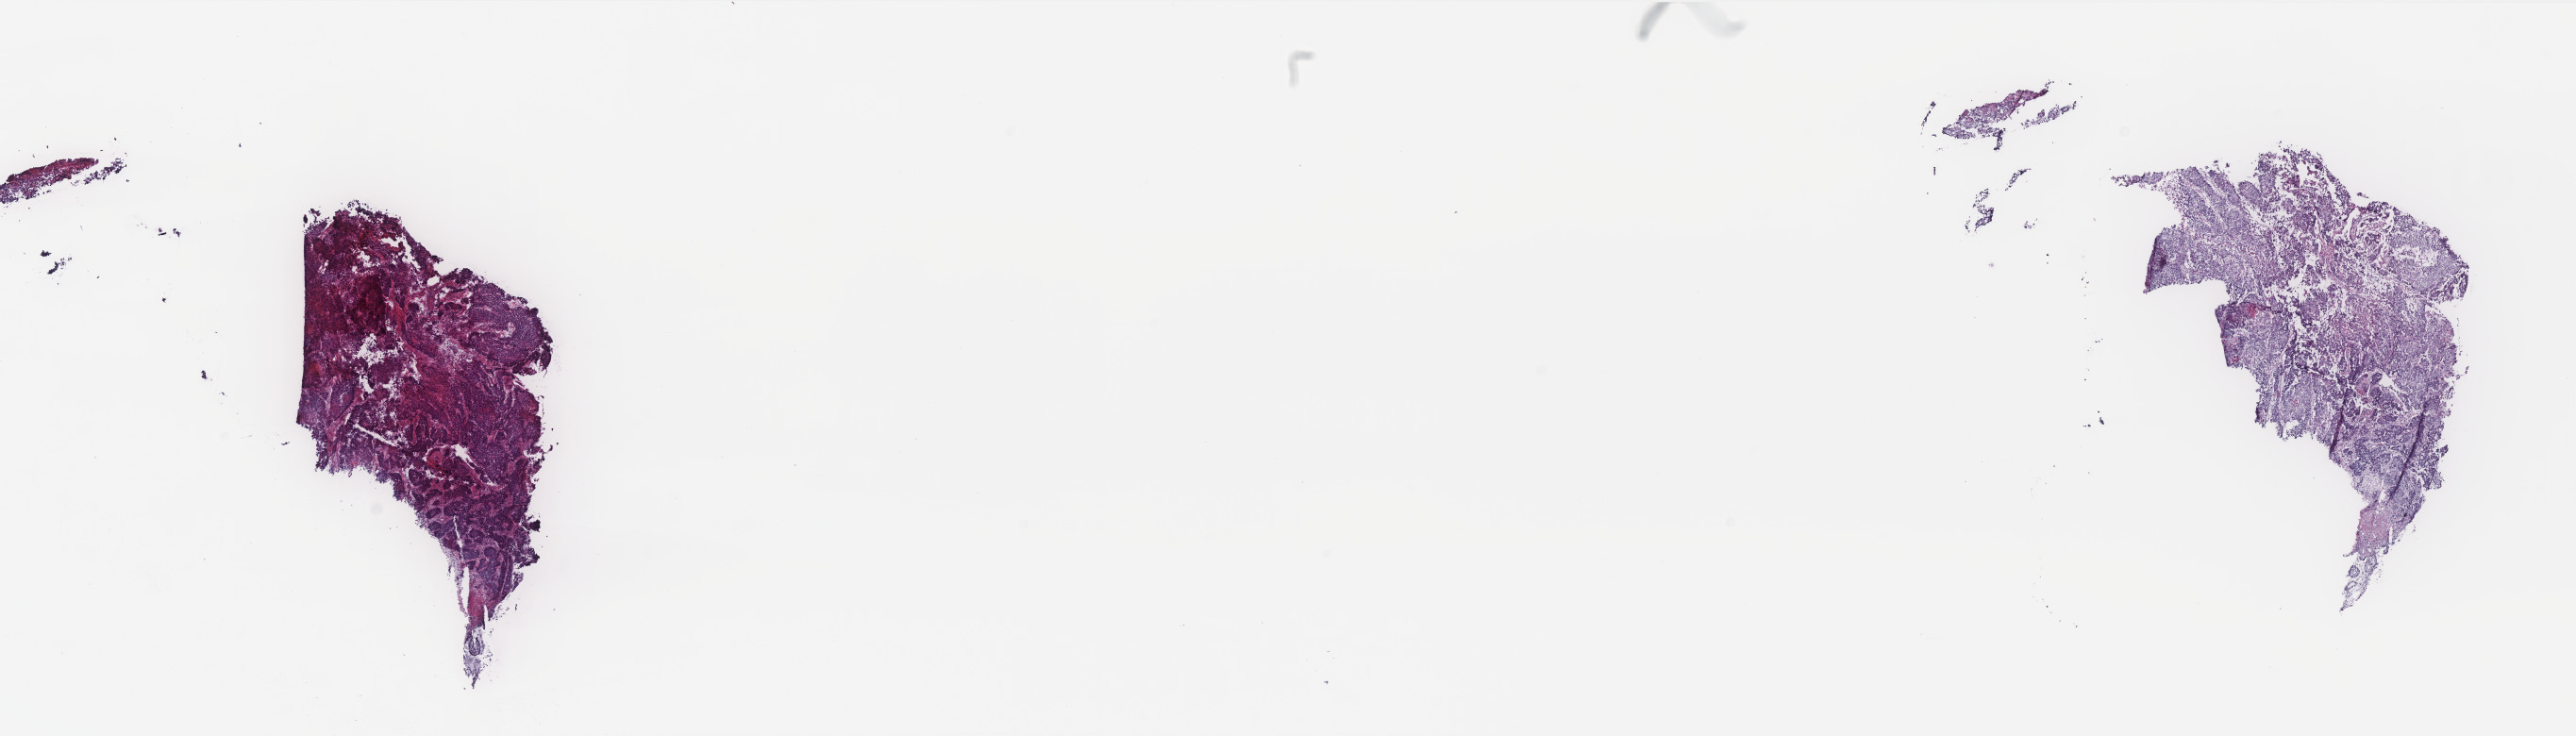
Whole-slide histology image, Hematoxylin and eosin (H&E) stained, whole scanned area (about 21.9 x 6.3 mm, from a 40x scan) shown as a low-resolution overview. Frozen section from the top of the tissue portion. Primary tumour sample from the cervix. Patient: female, age at initial diagnosis 49 years. Histologic grade: G3 (poorly differentiated). Pathologist review of this section (percent, as recorded): tumour cells 90%, tumour nuclei 90%, normal cells 0%, stromal cells 10%, necrosis 0%. Inflammatory infiltration, as recorded: lymphocyte infiltration 40%, monocyte infiltration 20%, neutrophil infiltration 20%.
* FIGO stage: IB2
* diagnosis: Squamous cell carcinoma, NOS (cervix uteri)